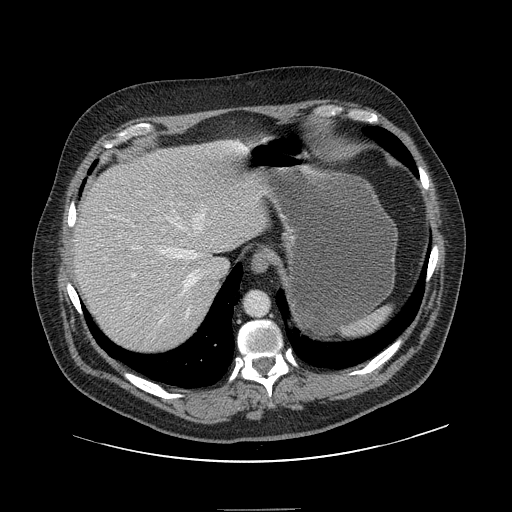
Contrast-enhanced abdominal CT, one axial slice; position 119 of 154 along the scan axis; intravenous contrast given; soft-tissue window (W 400 / L 40 HU); 2.5 mm slice thickness; 512 × 512 image matrix, field of view 451 × 451 mm. Male patient, age 61 years. Case-level facts recorded for this patient, not image findings: diagnosis: colorectal cancer liver metastases, imaged before liver resection; multiple liver metastases: yes; largest metastasis: 2.6 cm.
Outlined on this slice (outlined manually by an expert reader):
- hepatic veins: bounding box [x1, y1, x2, y2] px = [127, 211, 205, 324]
- liver: [73, 143, 268, 354]
- planned liver remnant (the part of the liver to remain after resection): [72, 143, 268, 351]
- portal vein (with intrahepatic branches): [110, 215, 156, 309]